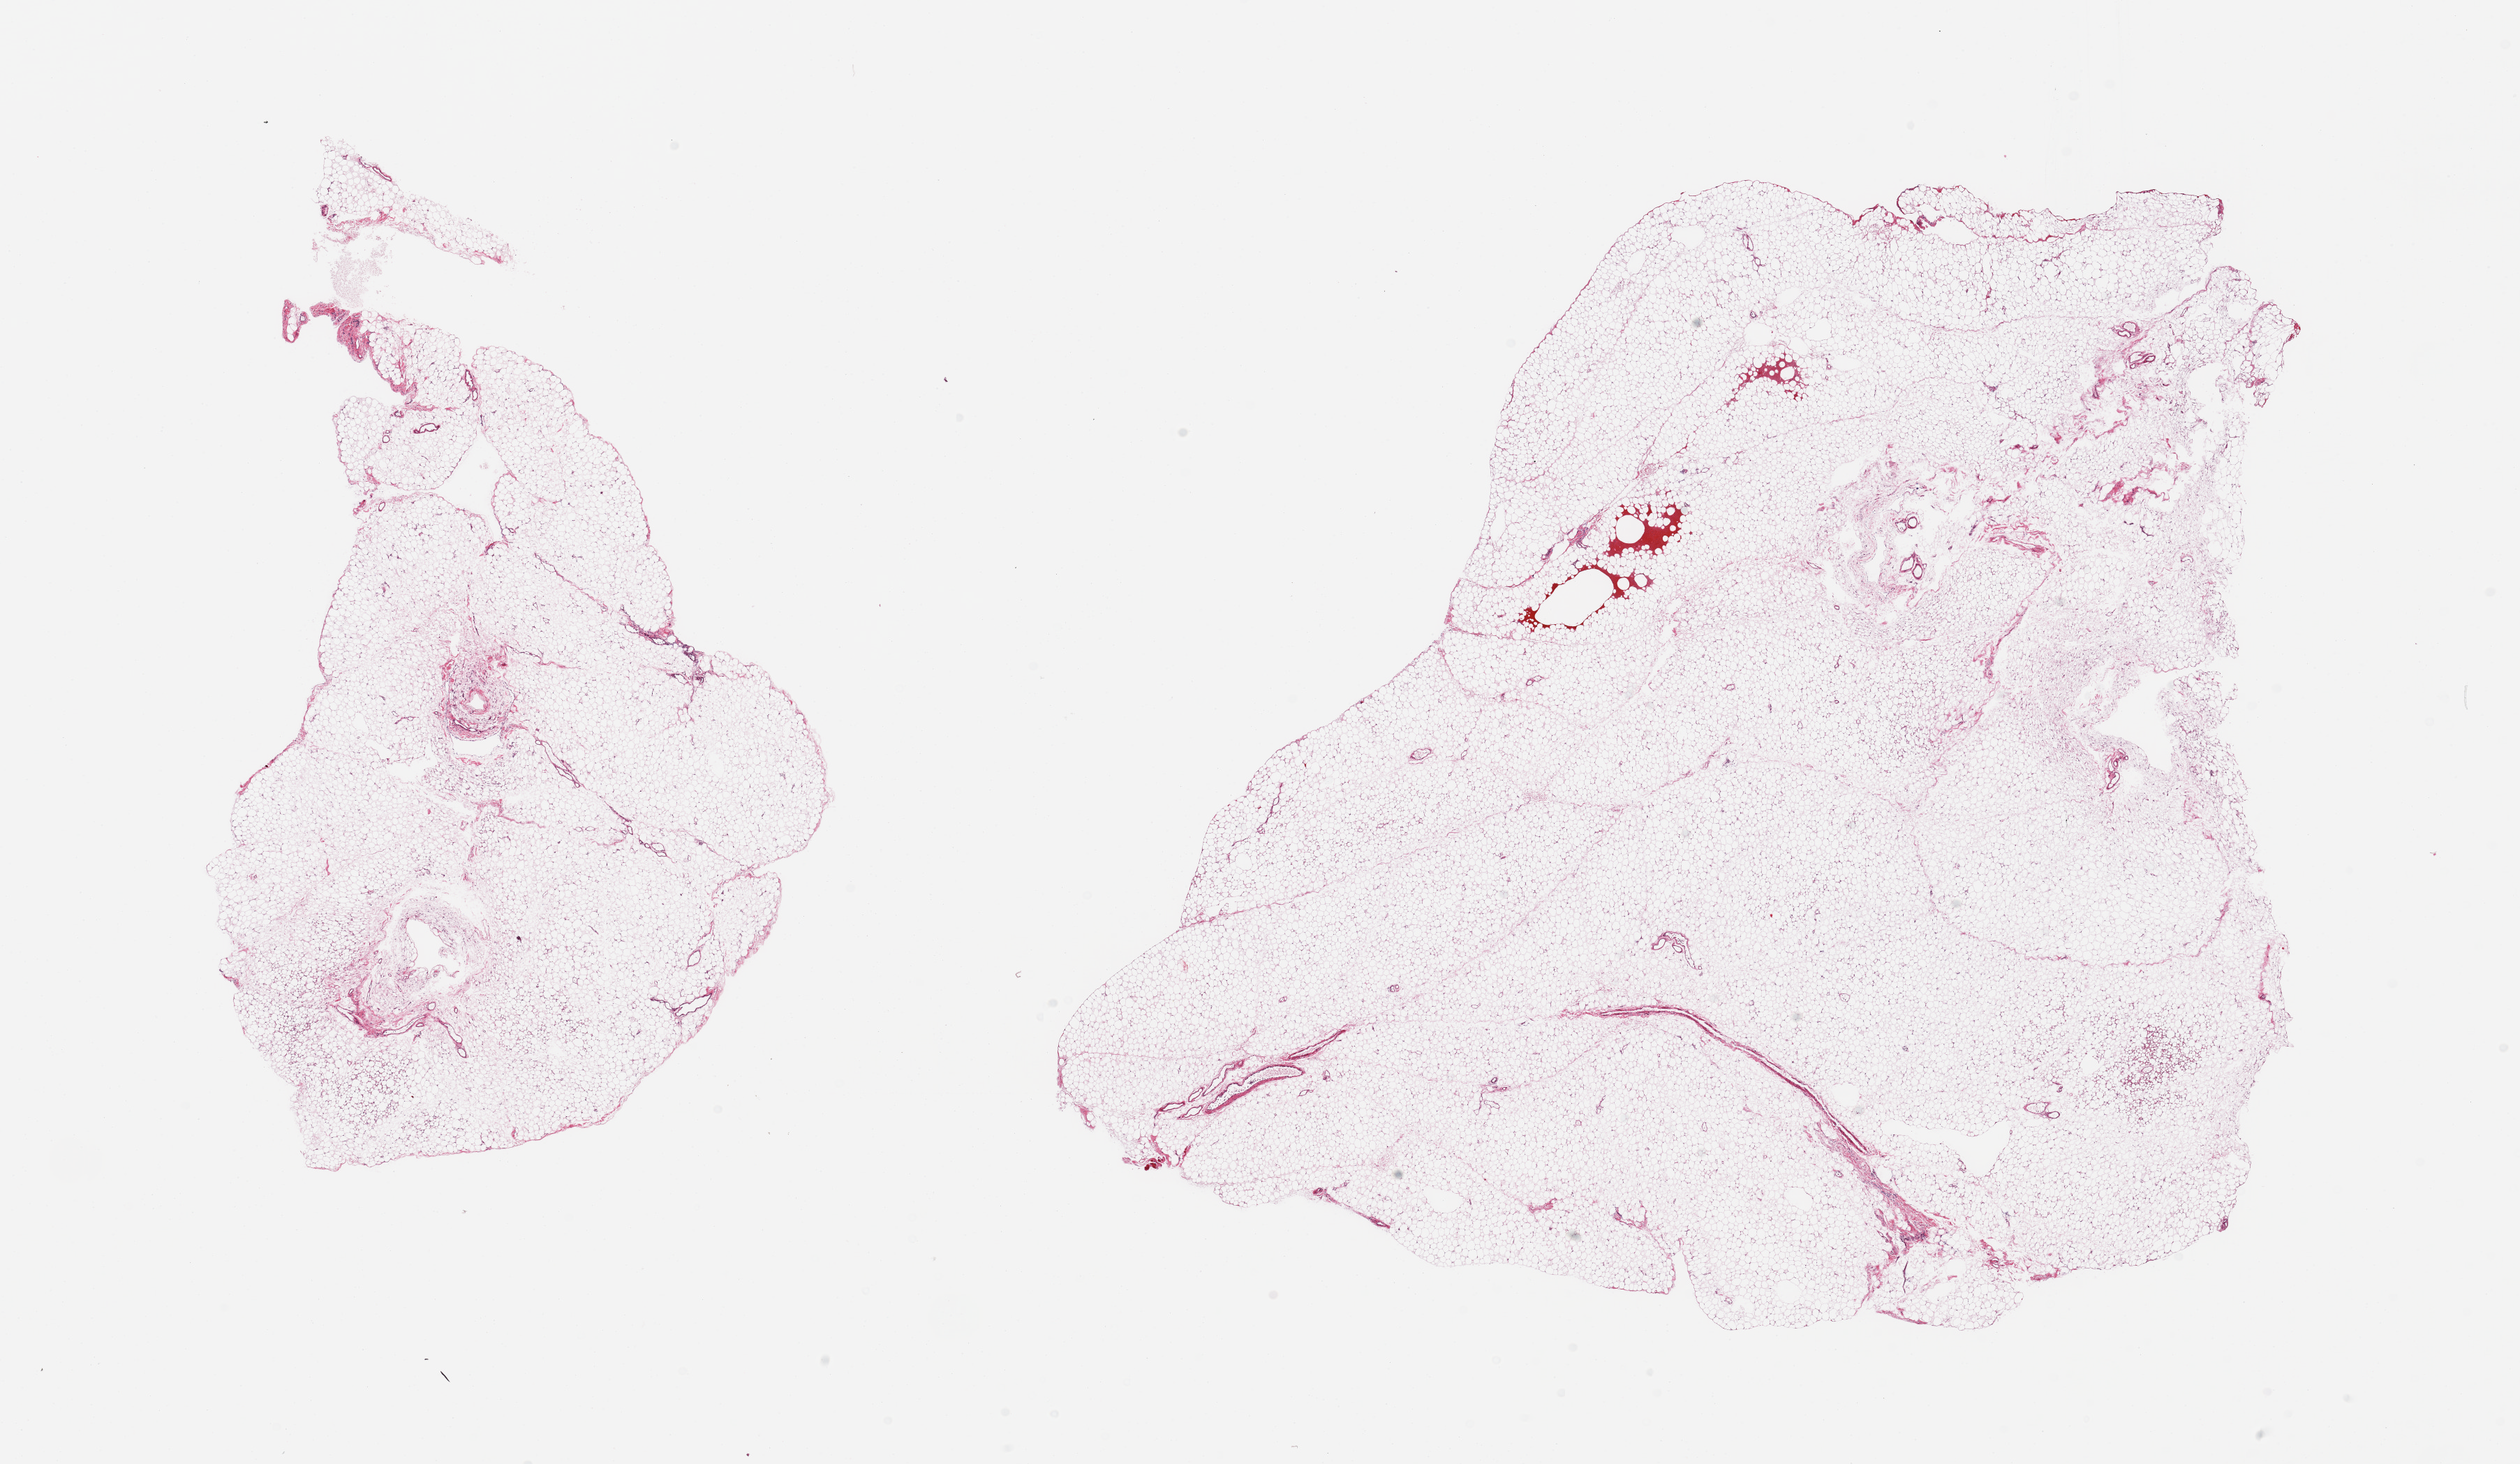
Whole-slide image, hematoxylin and eosin (H&E) stain — shown as a low-resolution overview of the whole scanned area (about 28.5 x 16.6 mm, slide scanned at 20x), PAXgene-fixed paraffin-embedded (PFPE) section, sampled site (target tissue): omentum, donor tissue sample. Donor sex: female.
Pathologist's review note for this sample: 2 pieces; 1% fibrous content.